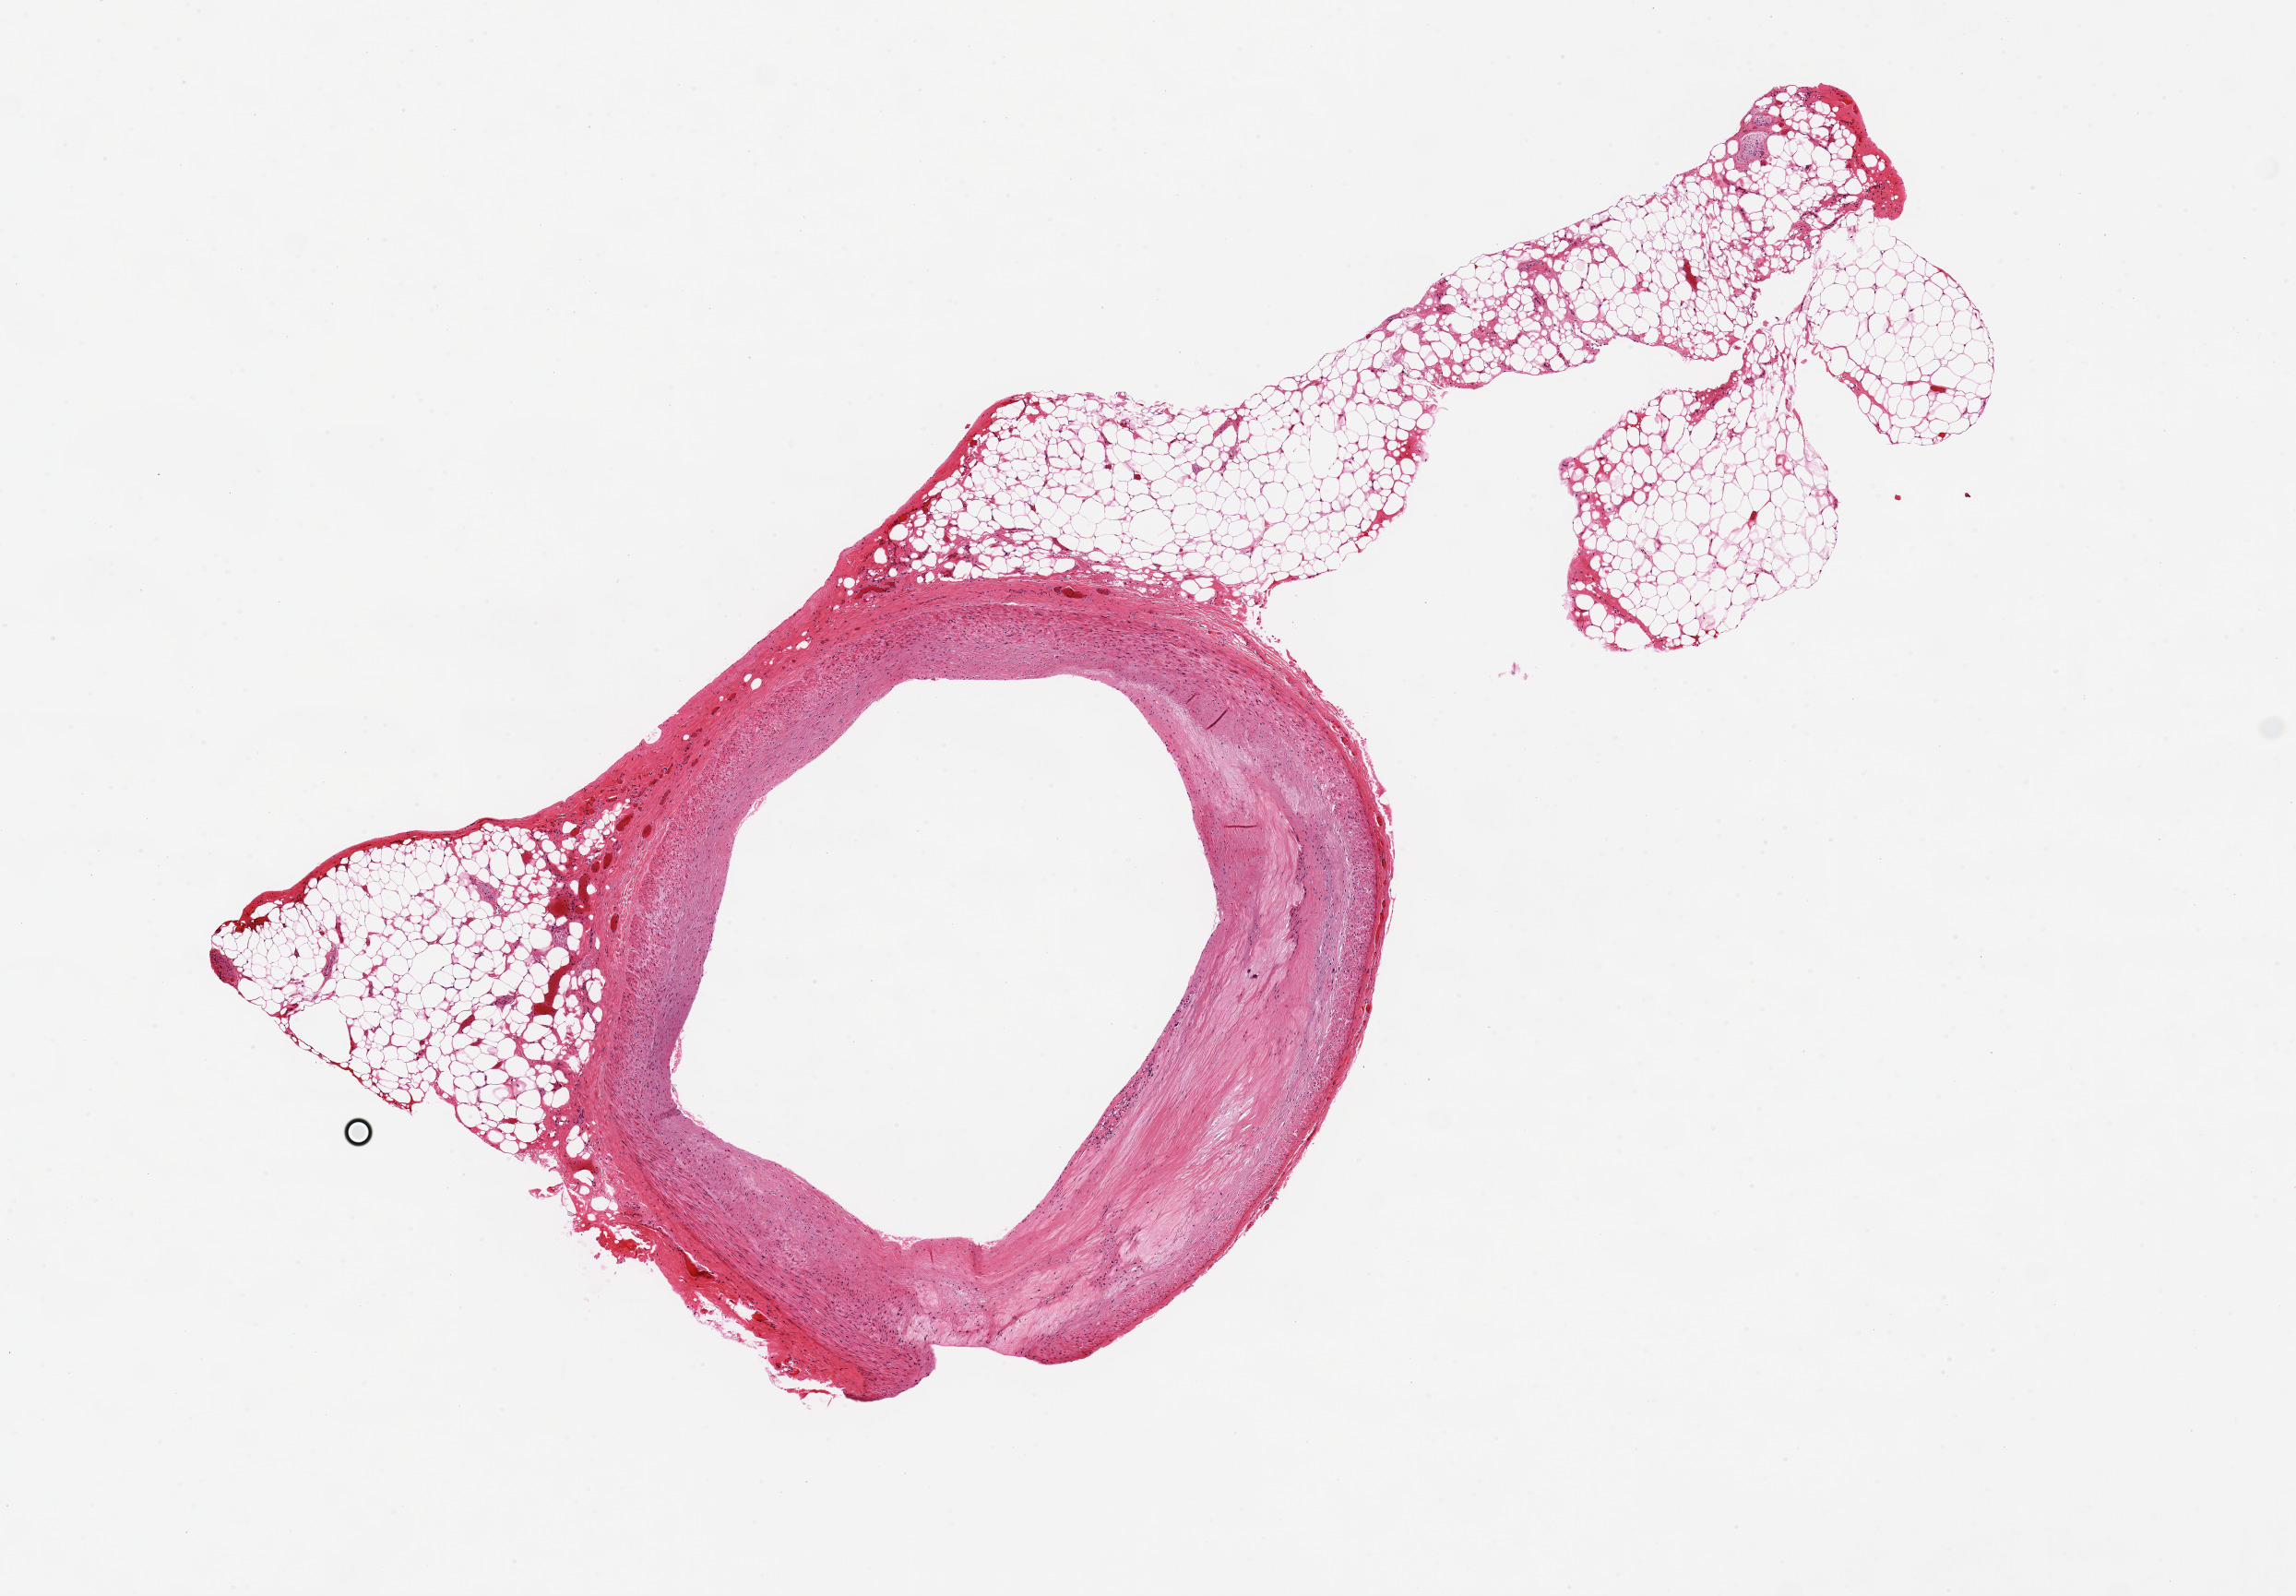
H&E whole-slide image, brightfield — a low-resolution overview of the entire scanned area, about 9.8 x 6.8 mm. PAXgene-fixed, paraffin-embedded tissue. Target tissue: coronary artery. Donor tissue sample. Donor sex: male.
Review note (as recorded): Fibrofatty plaque; wide lumen.